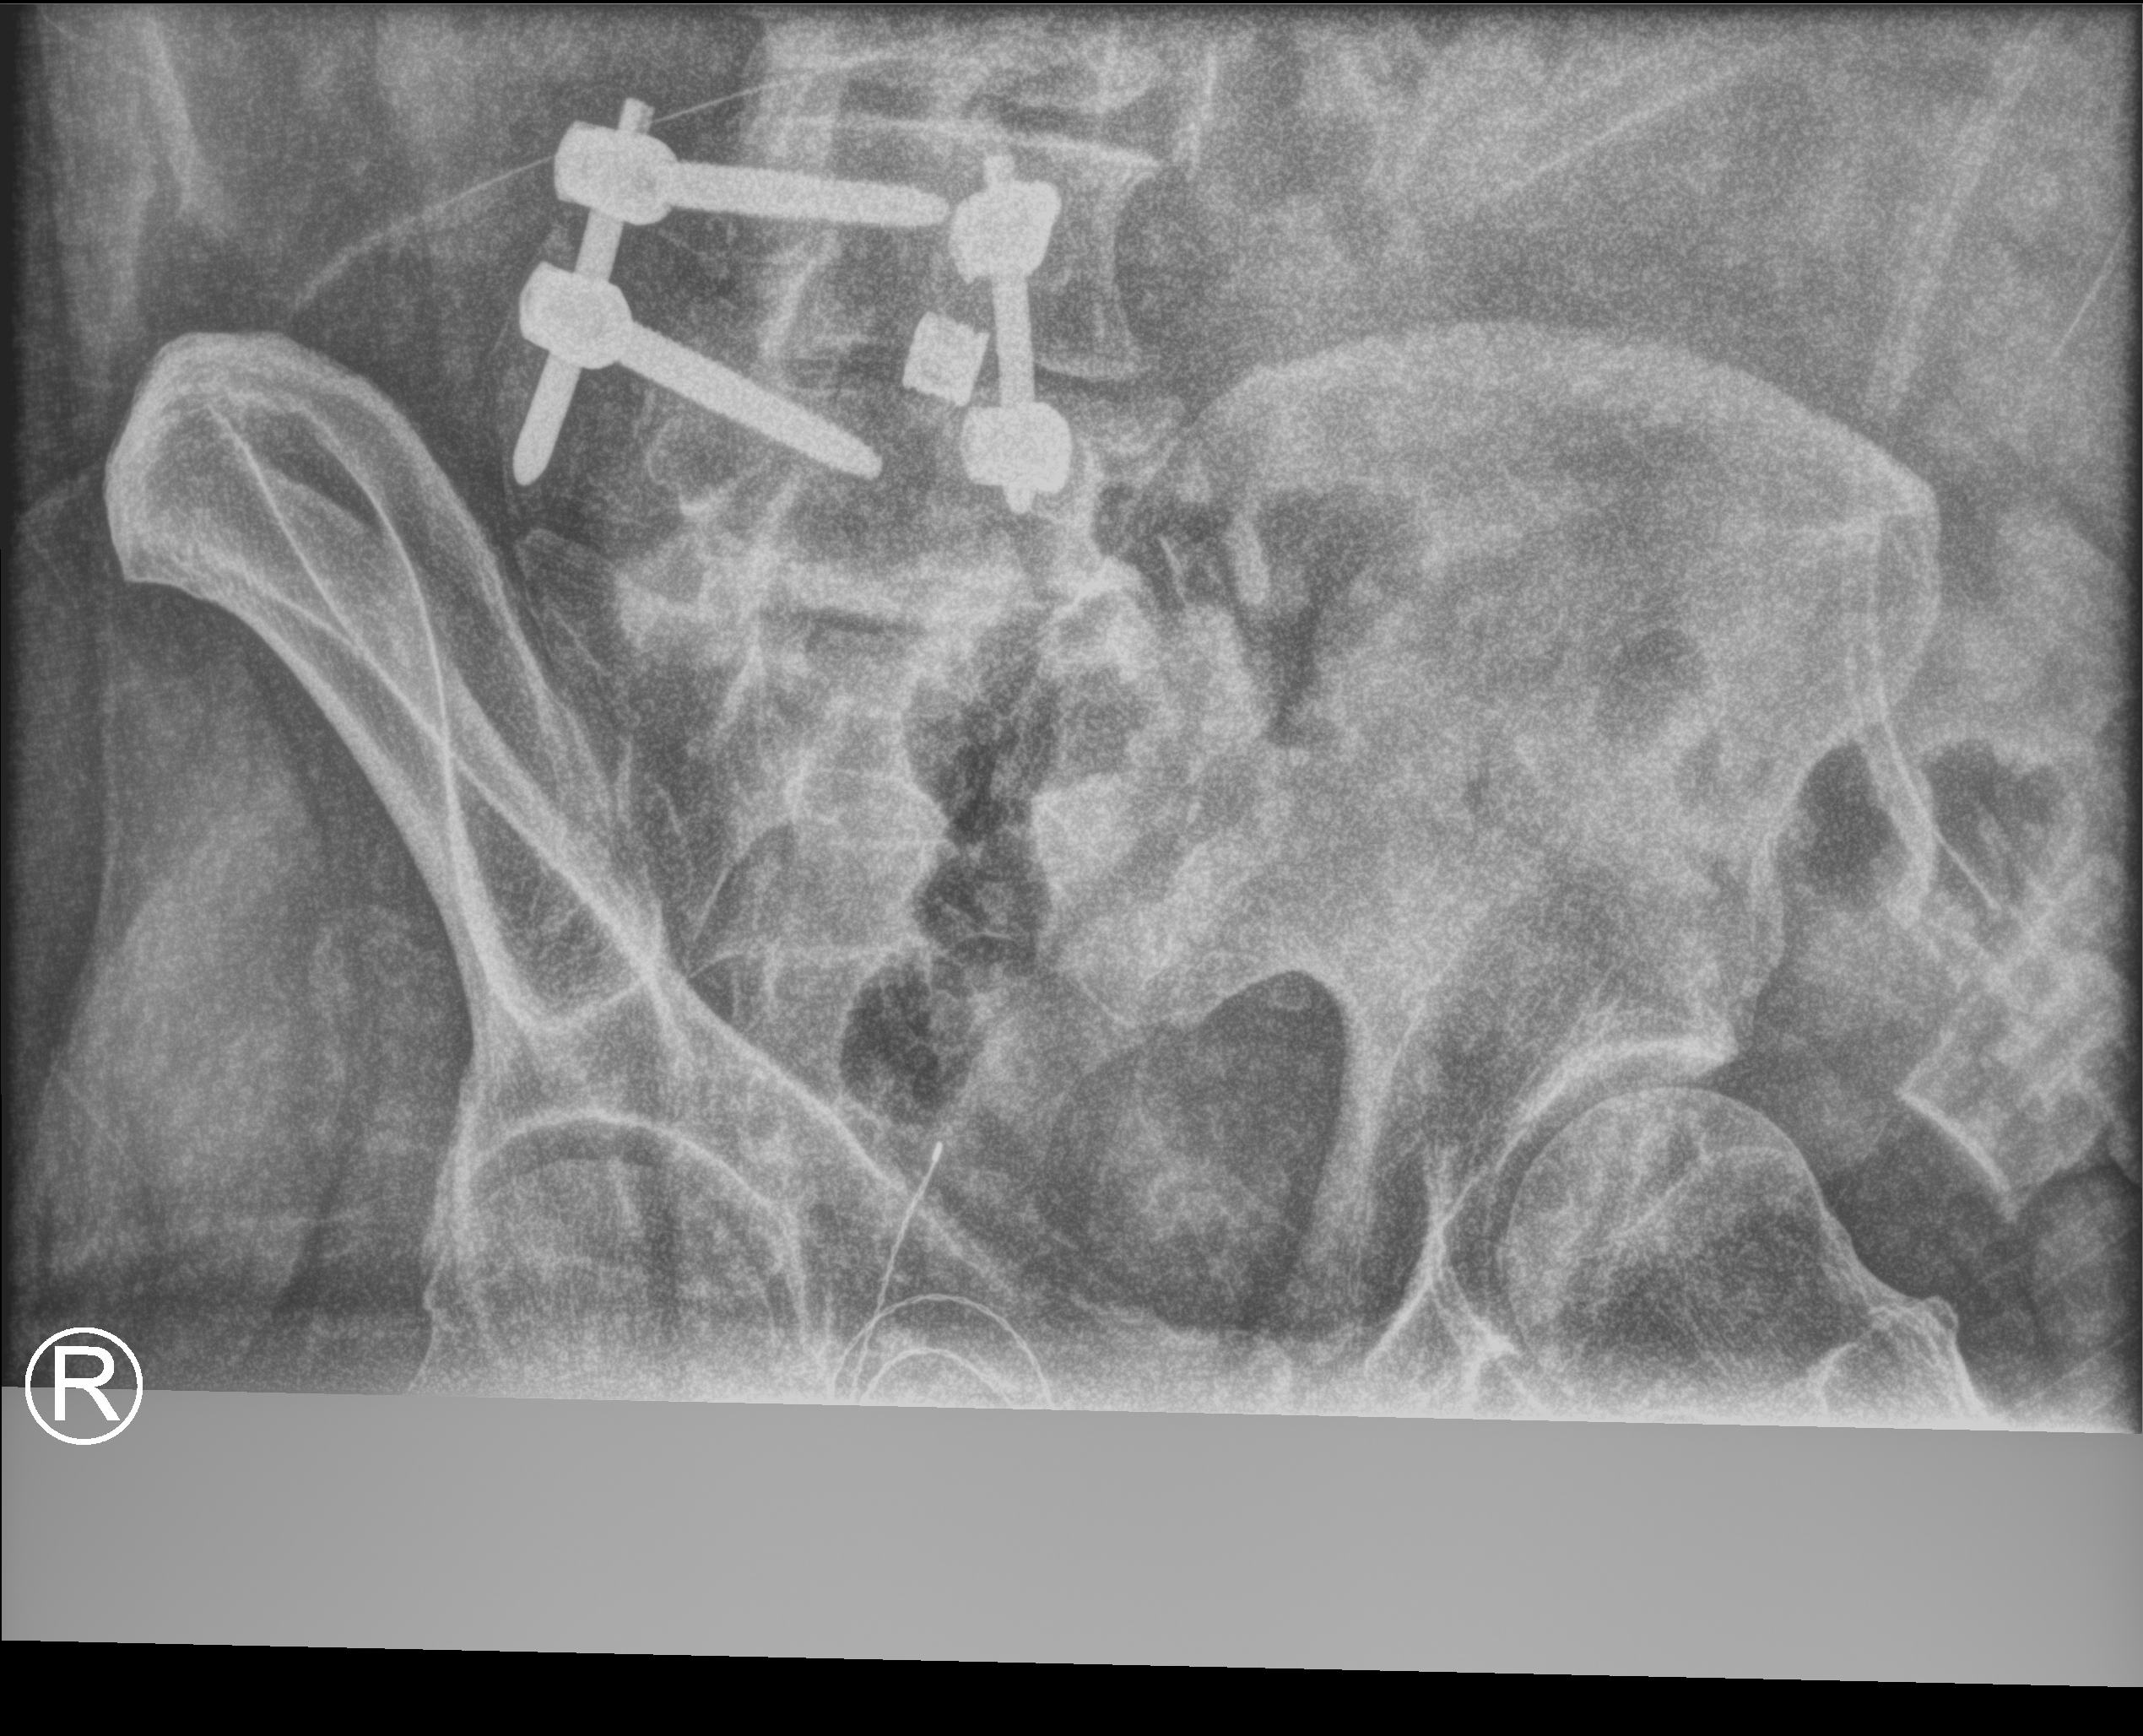
Portable abdomen radiograph, anteroposterior (AP) projection. Patient hospitalised with COVID-19; male, aged 60–74 years.
Admission-level facts for this patient (not findings on this image; timing relative to this image not recorded): mechanically ventilated during this hospital stay: yes; COPD (admission record): no.